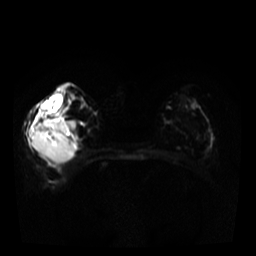
Breast MRI, one axial slice. Slice 16 of 34 in the series (ordered by position). Diffusion-weighted series; image 2 of 4 stored at this slice position (different b-values; order by instance number). 3 T. 5 mm slice thickness. 256 × 256 image matrix, field of view 320 × 320 mm. Female patient.
Outlined on this slice (outlined manually by an expert reader):
- tumour on diffusion-weighted imaging: bounding box <32,119,71,163> (left, top, right, bottom; pixels)